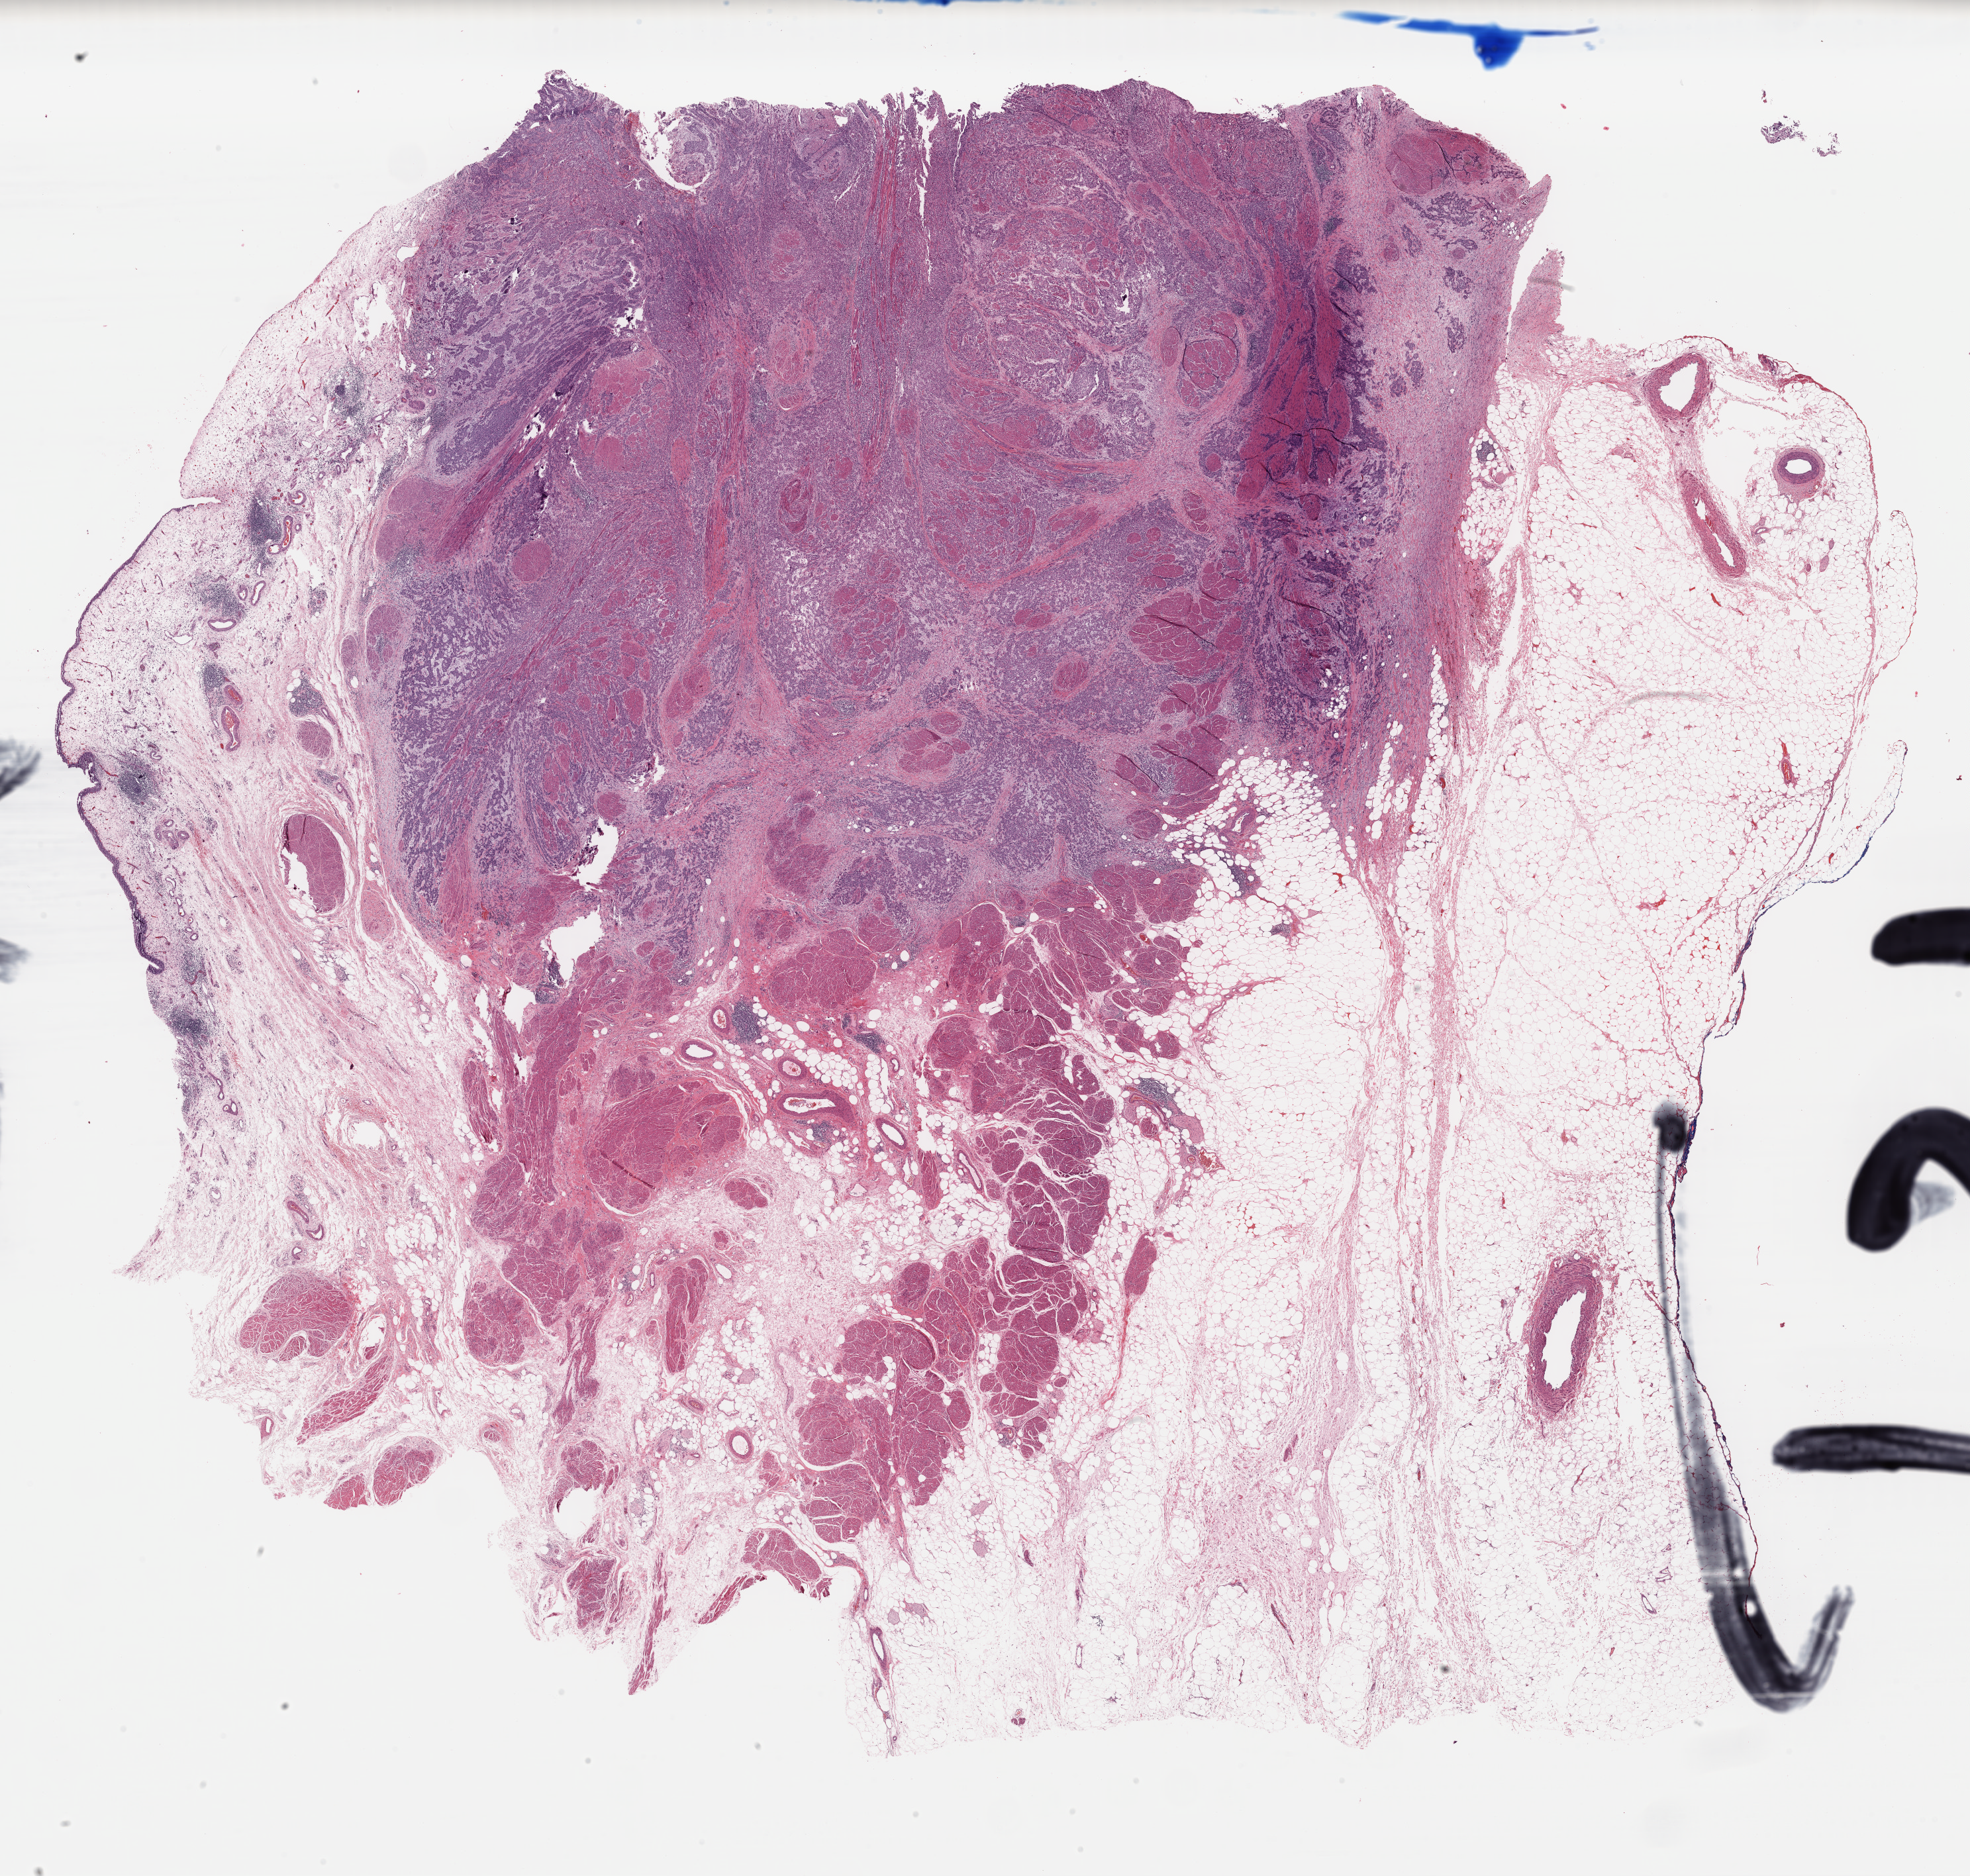
Digitized H&E-stained tissue section (whole slide) — whole scanned area (about 23.5 x 22.4 mm, acquisition: 40x scan) shown as a low-resolution overview; FFPE section; sample: primary tumour, bladder. Male, age 63 years at initial diagnosis. Histologic grade: high grade.
- histologic diagnosis: Transitional cell carcinoma
- AJCC pathologic stage: IV